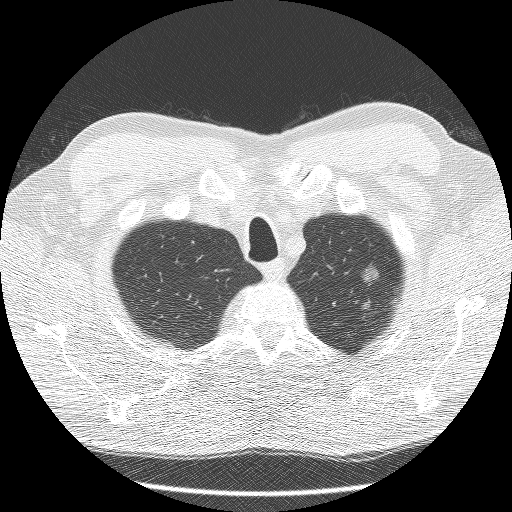
Low-dose screening chest CT, axial slice, third screening round (two years after baseline), lung window (W 1500 / L -600 HU), 2.5 mm slice thickness, 120 kVp, 512 × 512 image matrix, field of view 340 × 340 mm. Male participant, aged 60 years at enrolment. Former smoker at enrolment.
- Expert-annotated lung lesion, bounding box [x1, y1, x2, y2] px = [336, 253, 394, 300].
- The screening reader recorded 2 non-calcified nodules or masses ≥4 mm on this exam (right lower lobe, left upper lobe); which of them this box marks is not recorded.
- Official screen result: positive, other.